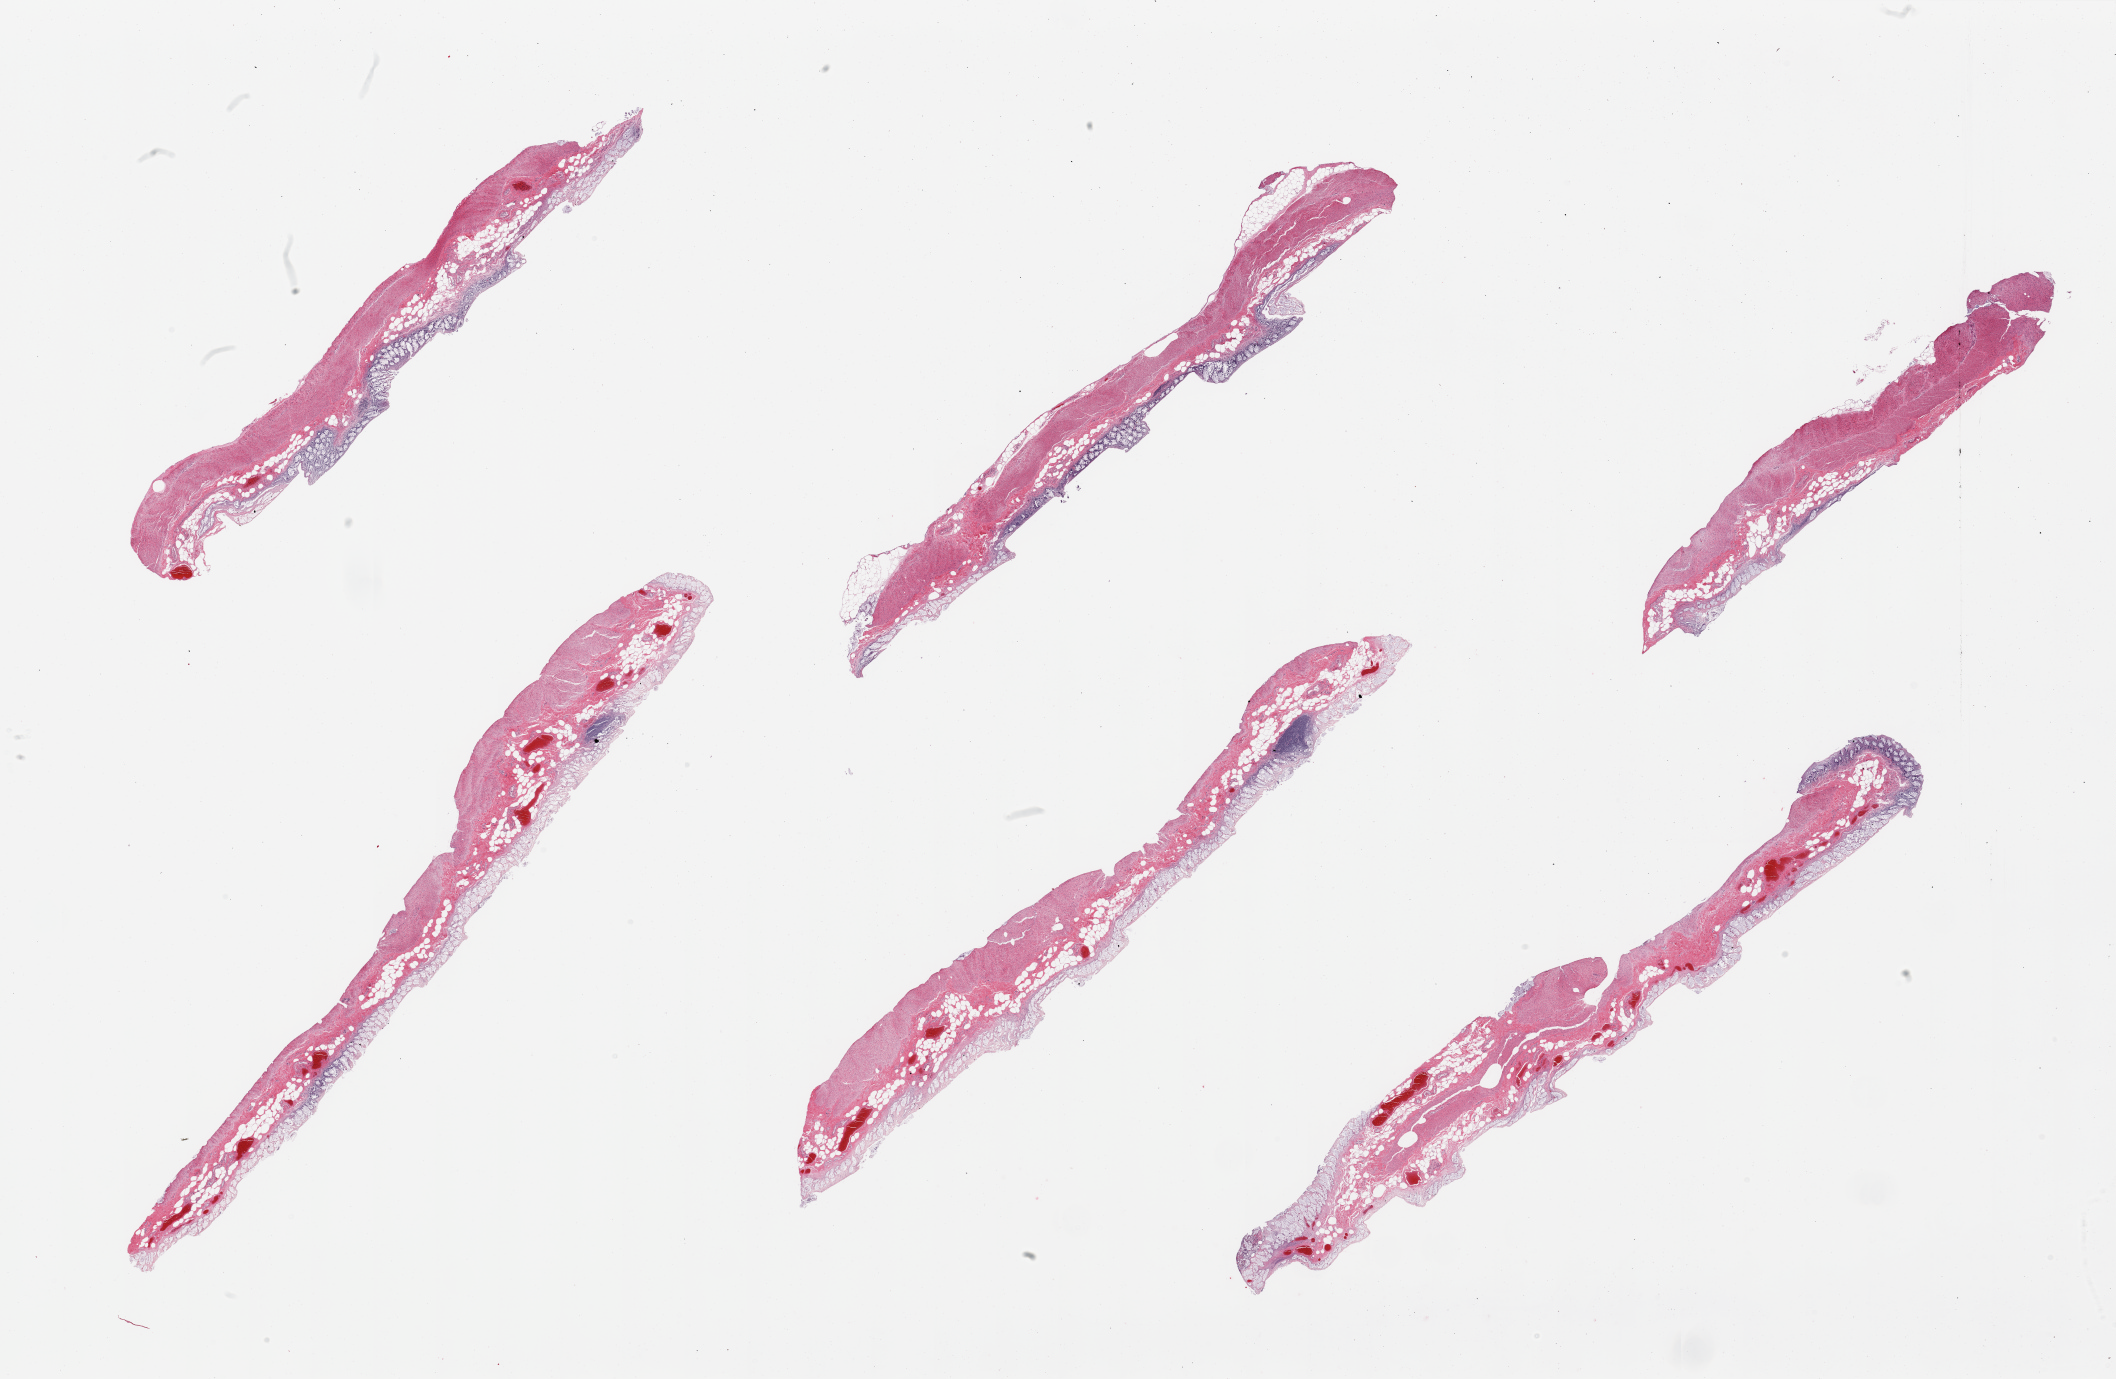
H&E whole-slide image, brightfield — low-resolution overview of the scanned area, about 33.5 x 21.8 mm (acquisition: 20x scan); PAXgene-fixed, paraffin-embedded tissue; section of transverse colon (target tissue); tissue donor sample. Male donor.
Review note (as recorded): 6 pieces; autolyzed.